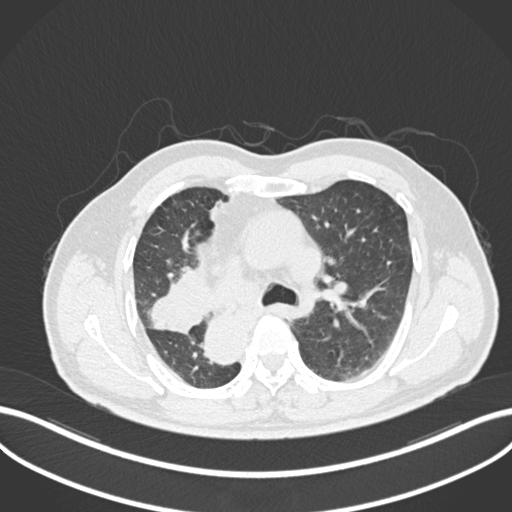
Chest CT, one axial slice. Slice 155 of 206 in the series (ordered by position). Reconstruction kernel B30f. Lung window (W 1500 / L -600 HU). 1 mm slice thickness. 512 × 512 image matrix, field of view 400 × 400 mm. Male patient, age 67 years. Case-level facts recorded for this patient, not image findings: clinical TNM (as recorded): T2a N0 M0.
Annotated regions visible in this slice (rectangle marked by the reading radiologist):
- lung tumour (recorded histology: squamous cell carcinoma): bounding box (x1, y1, x2, y2) in pixels: (144, 273, 210, 337)